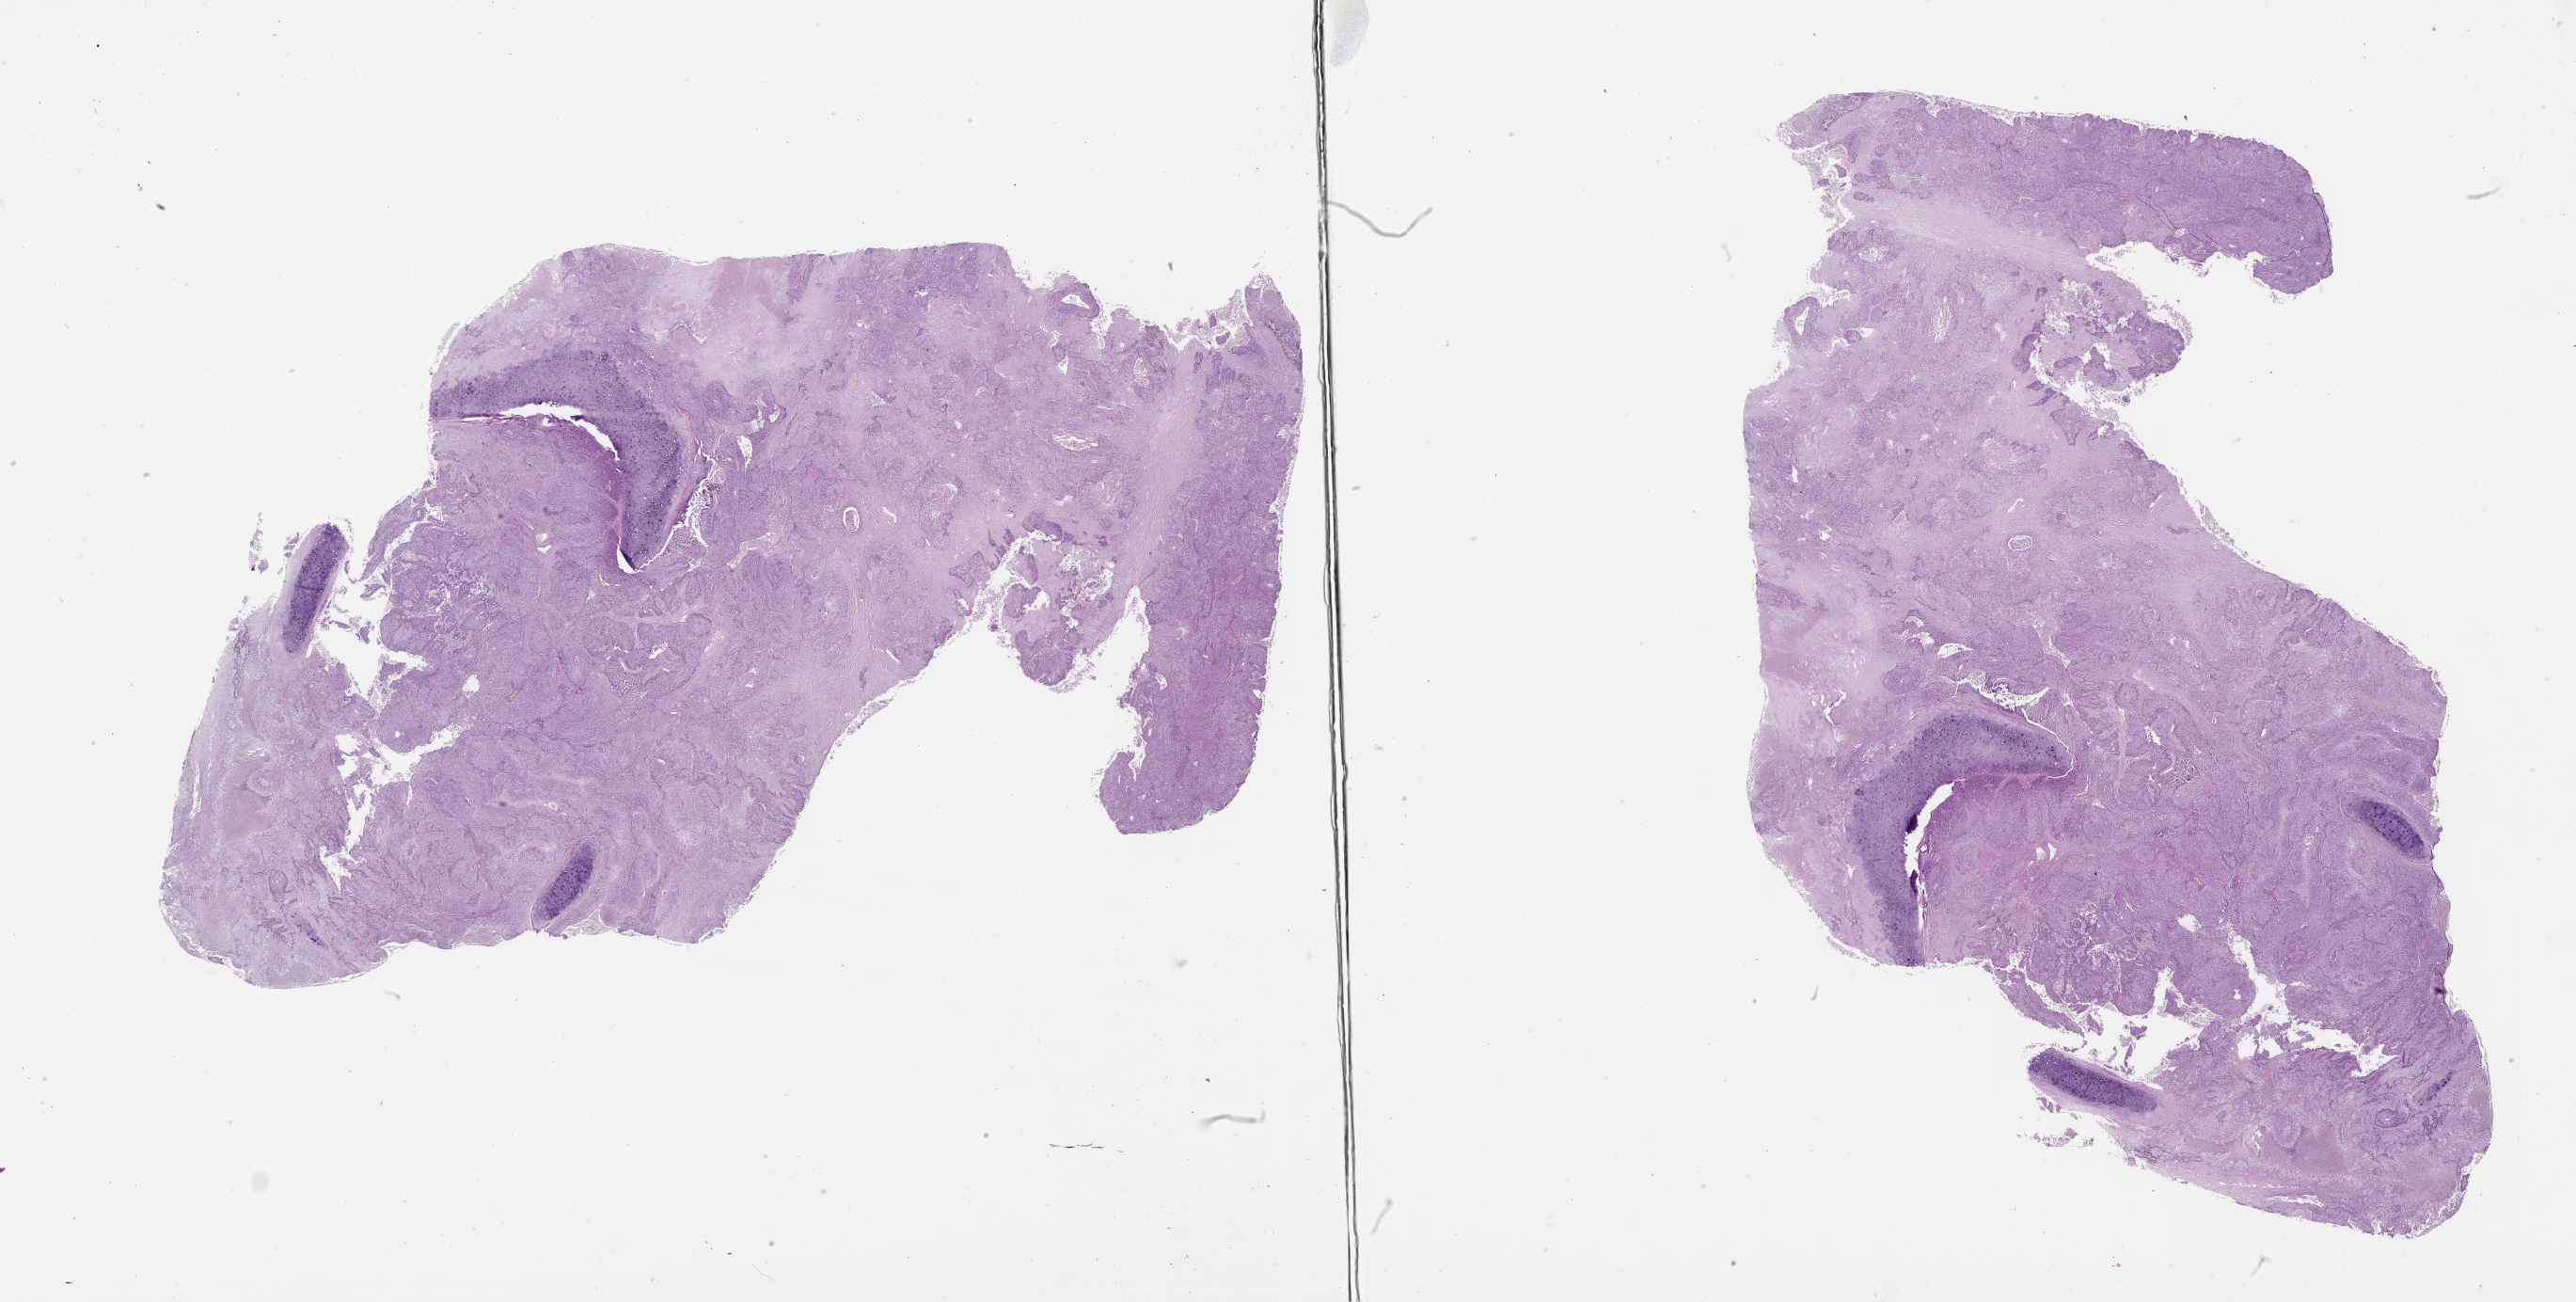
Digitized H&E-stained tissue section (whole slide), shown as a low-resolution overview of the whole scanned area (about 44.1 x 22.3 mm, slide scanned at 20x); tumour tissue sample, lung. Male, 65 y/o.
* patient diagnosis (cohort enrolment): squamous cell carcinoma (lung)